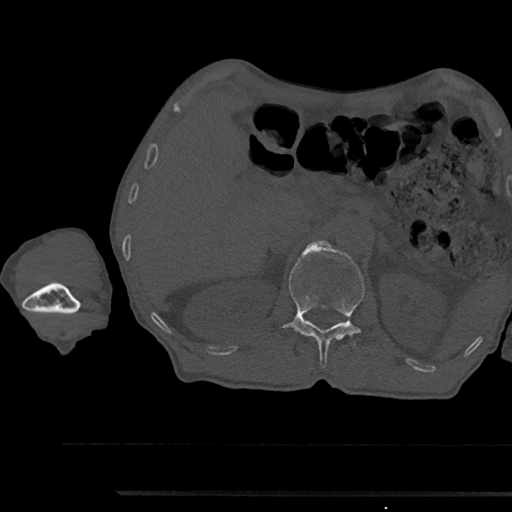
CT including the spine, one axial slice. Slice 637 of 797 in the series (ordered by position). Reconstruction kernel Br40s/3. Bone window (W 1800 / L 400 HU). 0.5 mm slice thickness. 512 × 512 image matrix, field of view 367 × 367 mm. Male patient, age 79 years. From the clinical record (not read from this slice): primary cancer: prostate.
Annotated regions visible in this slice (semi-automatic segmentation, software-assisted and operator-edited):
- L1 vertebra: bounding box <284,241,365,367> (left, top, right, bottom; pixels)